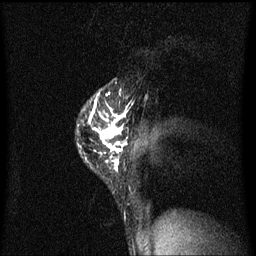
Breast MRI (dynamic contrast-enhanced), one sagittal slice. Position 47 of 60 along the scan axis. Dynamic contrast-enhanced series, image 2 of 3 at this slice position (ordered by acquisition). 1.5 T. TE 4.2 ms, TR 8.4 ms. 2 mm slice thickness. 256 × 256 image matrix, field of view 200 × 200 mm. Female patient, age 40 years.
Outlined on this slice (semi-automatically segmented with operator editing):
- analysis volume of interest (the breast-tissue region the enhancement analysis was run in; not a lesion): box from (x=79, y=90) to (x=131, y=171) px
- tumour enhancement mask (voxels above the 70 % enhancement threshold inside the analysis volume of interest): (x=91, y=92)–(x=130, y=171)